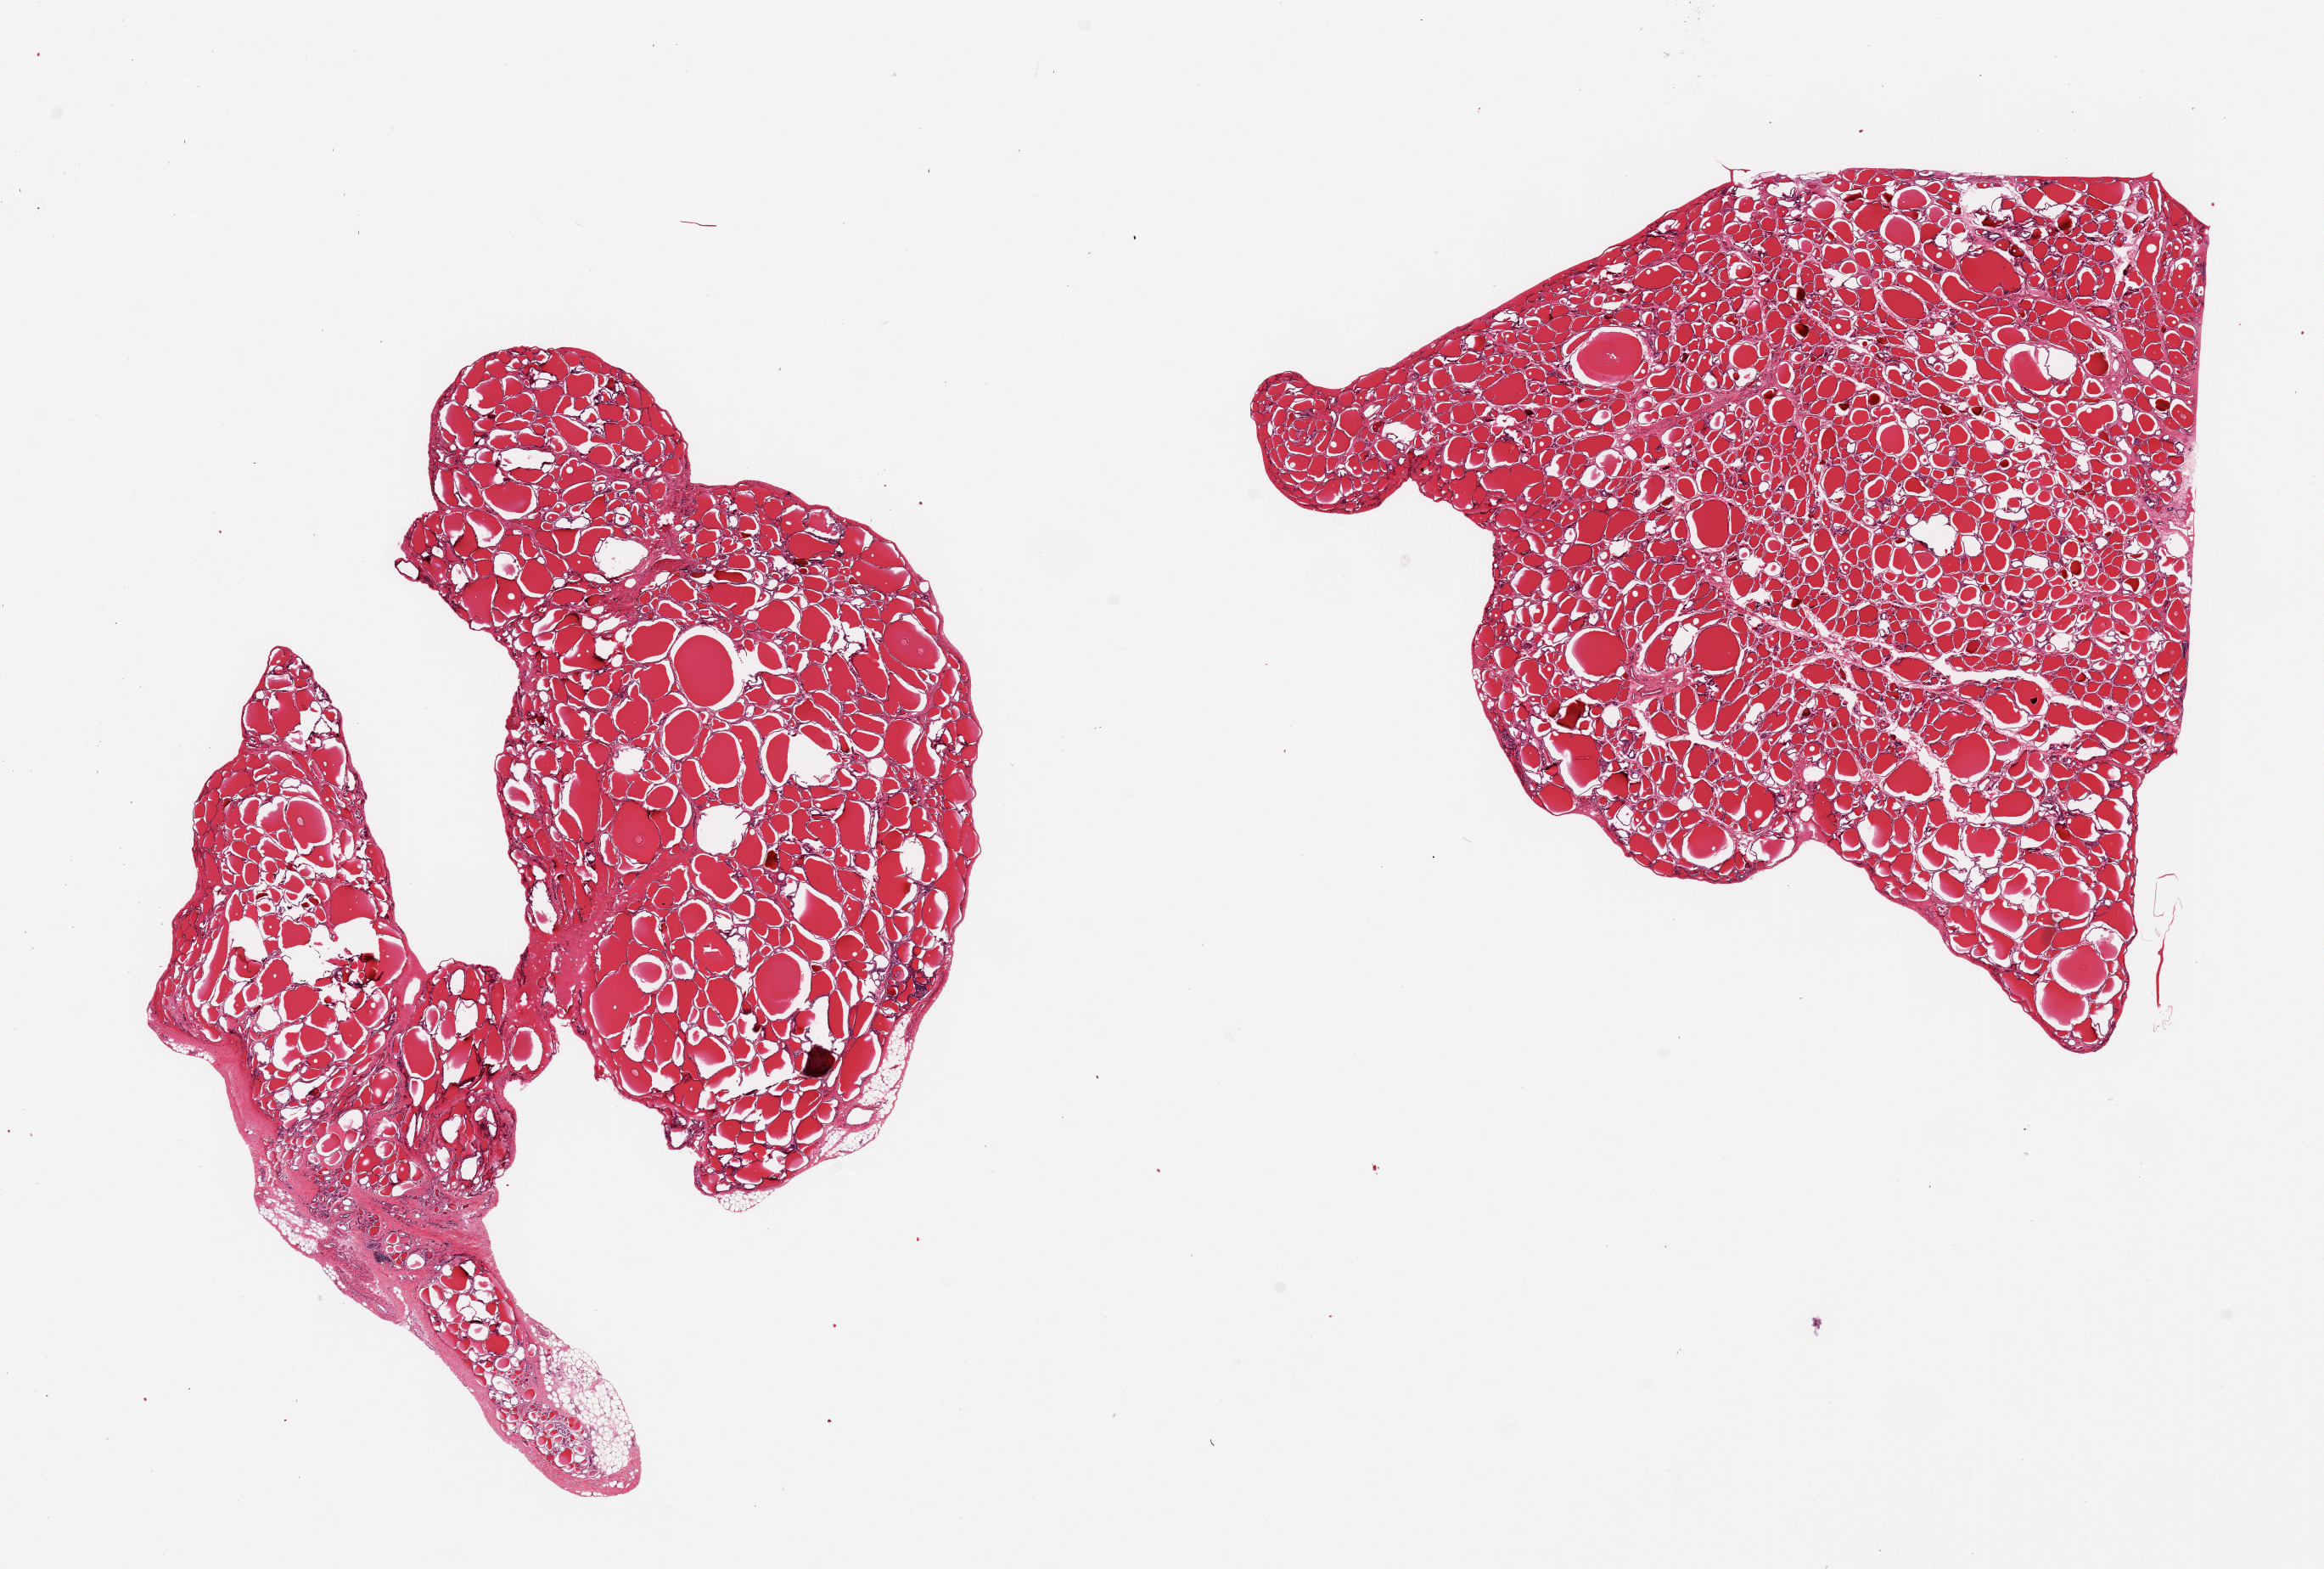
Hematoxylin and eosin (H&E) whole-slide image, brightfield — shown as a low-resolution overview of the whole scanned area (about 21.7 x 14.6 mm, slide scanned at 20x). PAXgene-fixed paraffin-embedded (PFPE) section. Sampled site (target tissue): thyroid. Tissue donor sample. Female donor.
• reviewer comment on this tissue sample: 2 pieces, 8x8 & 9x8mm